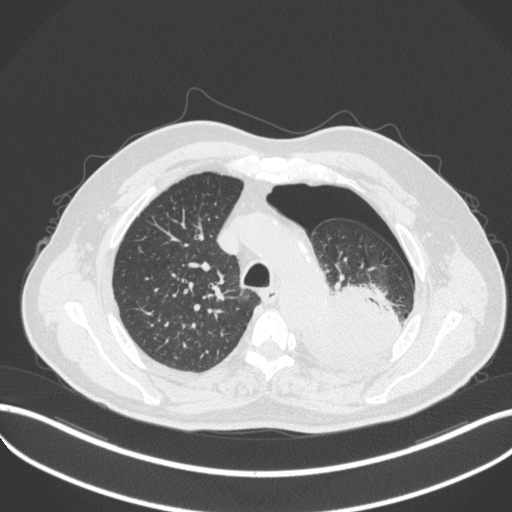
Chest CT, one axial slice. Slice 382 of 466 in the series (ordered by position). Reconstruction kernel B31f. 120 kVp. Lung window (W 1500 / L -600 HU). 512 × 512 image matrix, field of view 400 × 400 mm. Male patient, age 76 years. From the clinical record (not read from this slice): clinical TNM (as recorded): T3 N0 M1b.
Annotated regions visible in this slice (bounding box drawn by a radiologist):
- lung tumour (recorded histology: adenocarcinoma): bounding box [x1, y1, x2, y2] px = [303, 282, 405, 373]